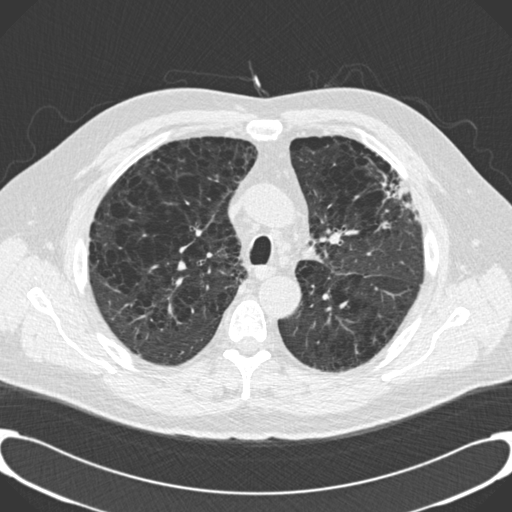
Axial slice from a low-dose chest CT screening exam; third annual screen; lung window (W 1500 / L -600 HU); 2 mm slice thickness; 120 kVp; slice 49 of 189 in the series; 512 × 512 image matrix. Male participant, aged 59 years at enrolment. Current smoker at enrolment.
- Lesion marked by an expert reader, bounding box (x1, y1, x2, y2) in pixels: (358, 150, 419, 221).
- No non-calcified nodule or mass ≥4 mm was recorded by the screening reader at this exam.
- Official screen result: positive, other.